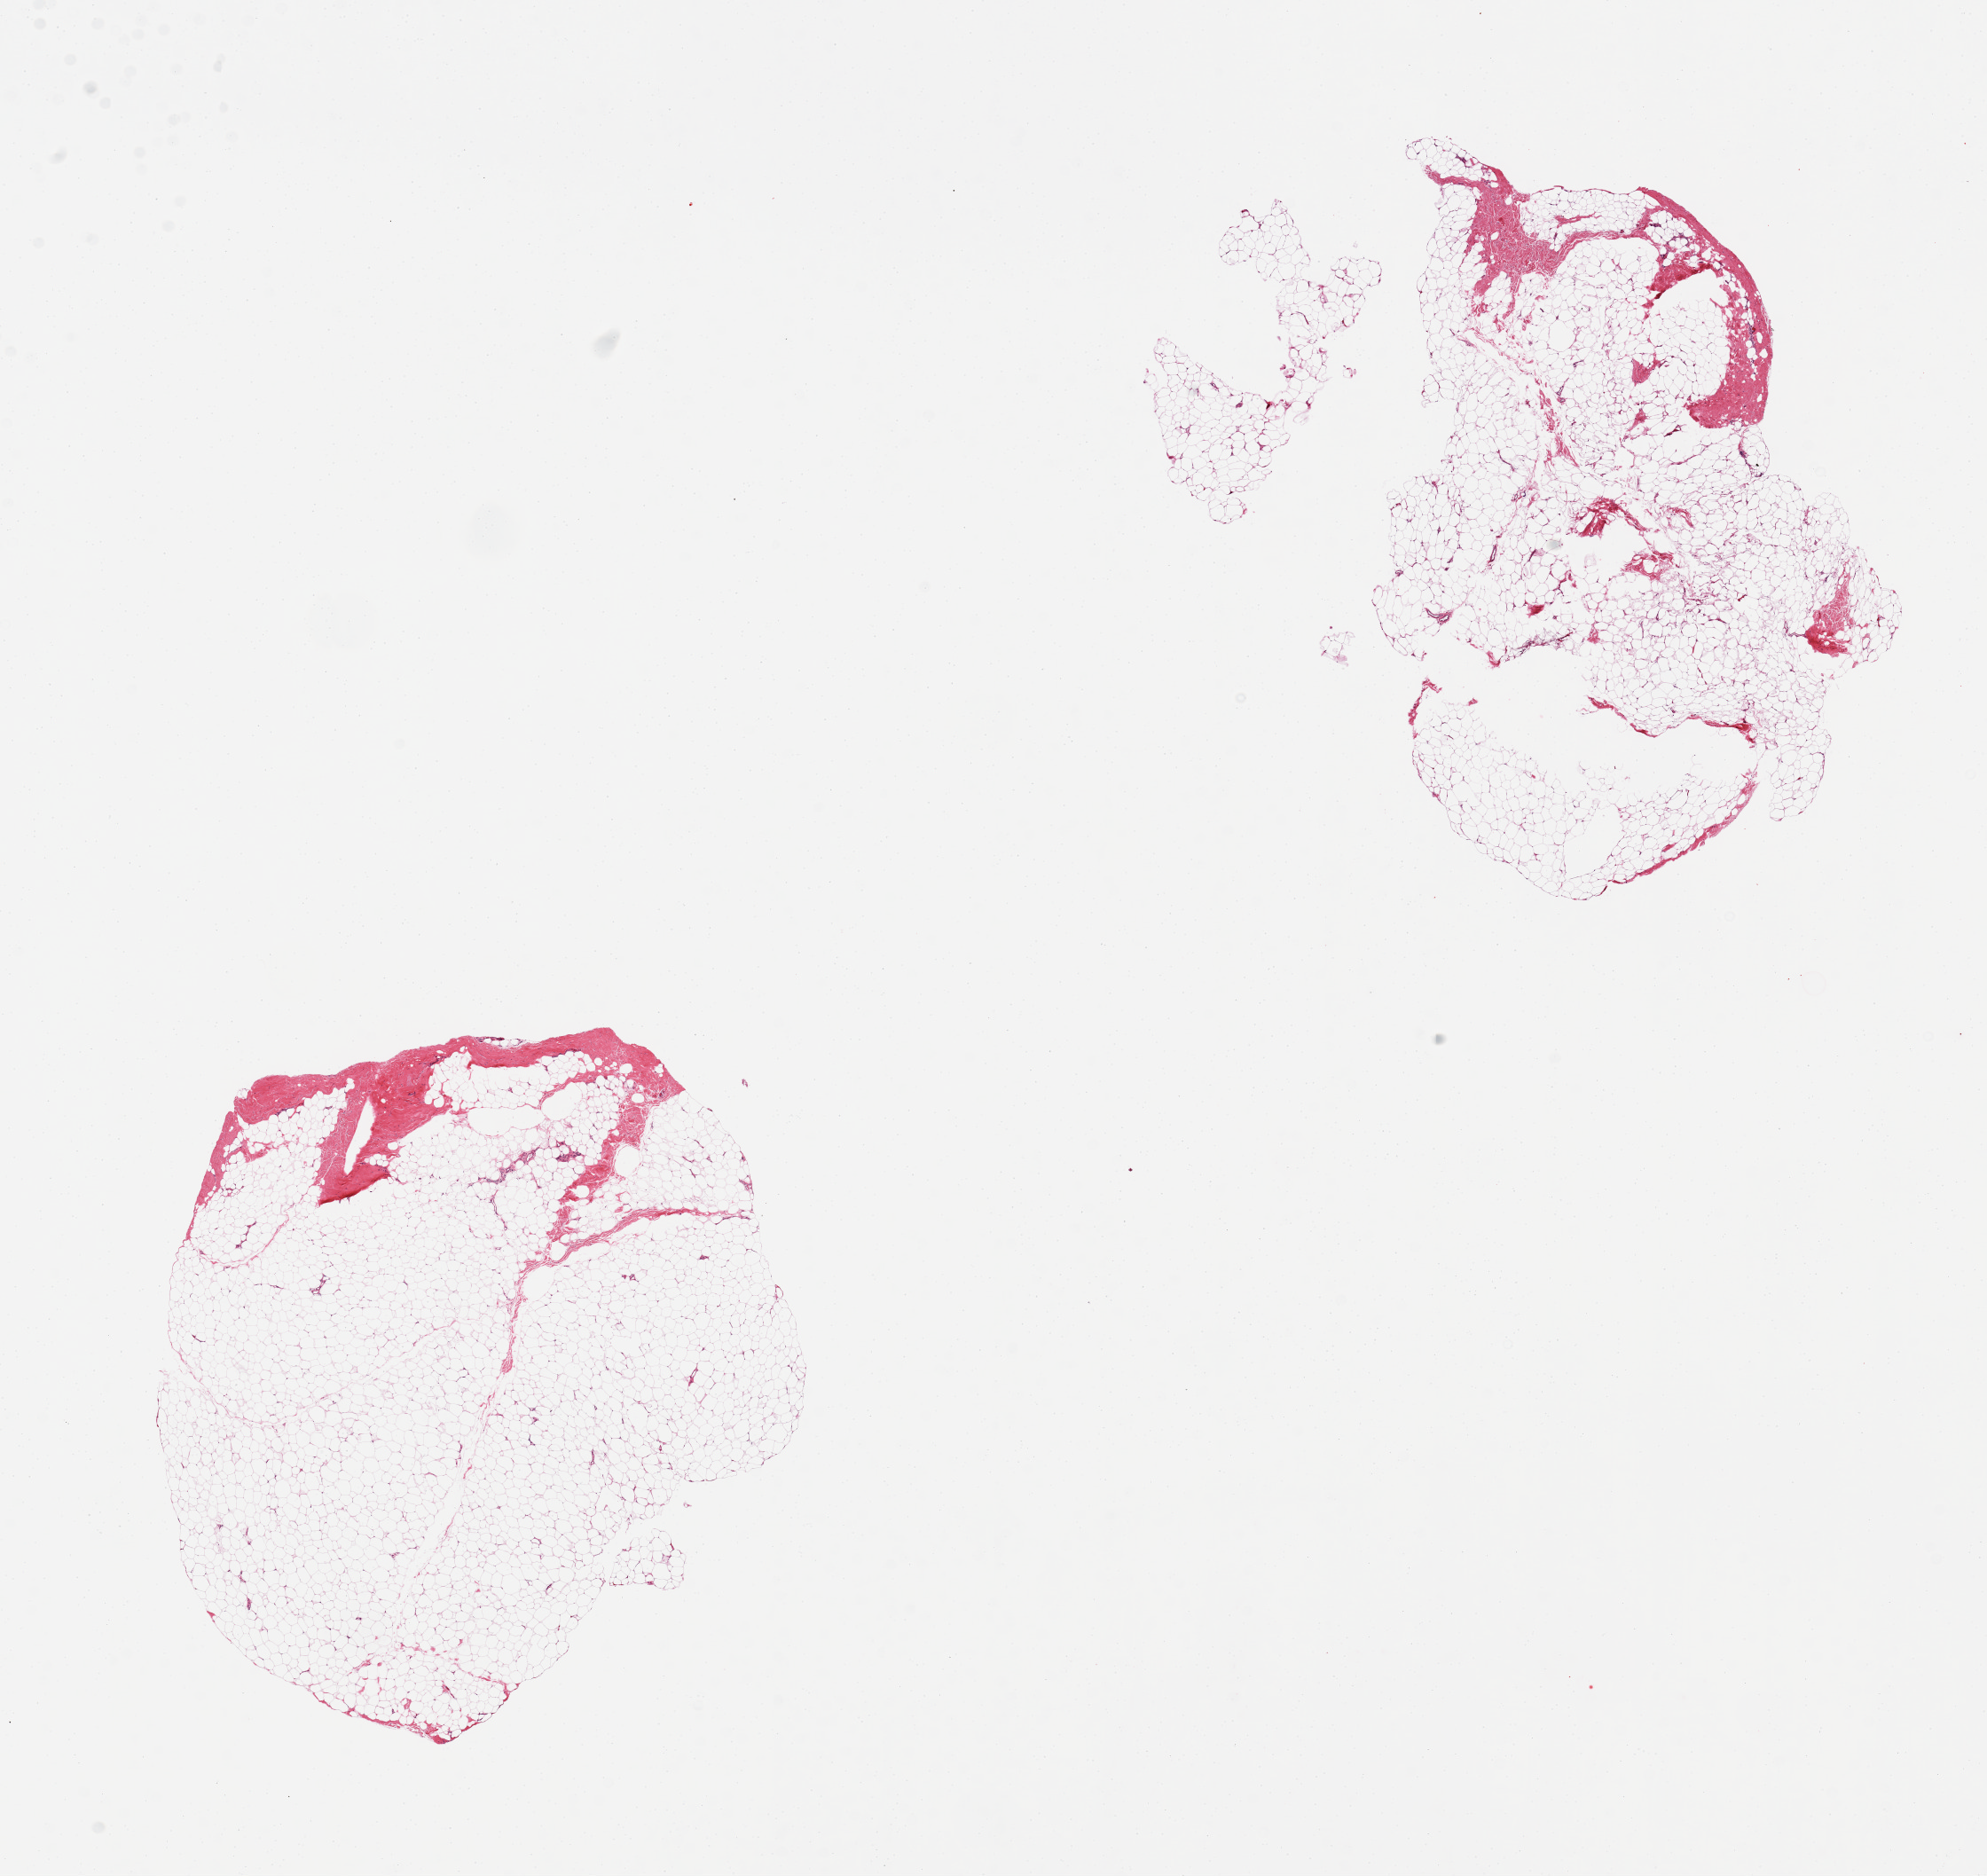
Whole-slide image, haematoxylin and eosin stain — whole scanned area (about 17.7 x 16.7 mm) shown as a low-resolution overview; PAXgene-fixed, paraffin-embedded tissue; section of breast (target tissue); tissue donor sample. Donor sex: male.
Pathologist's review note for this sample: 2 pieces, ~10% fibrous.